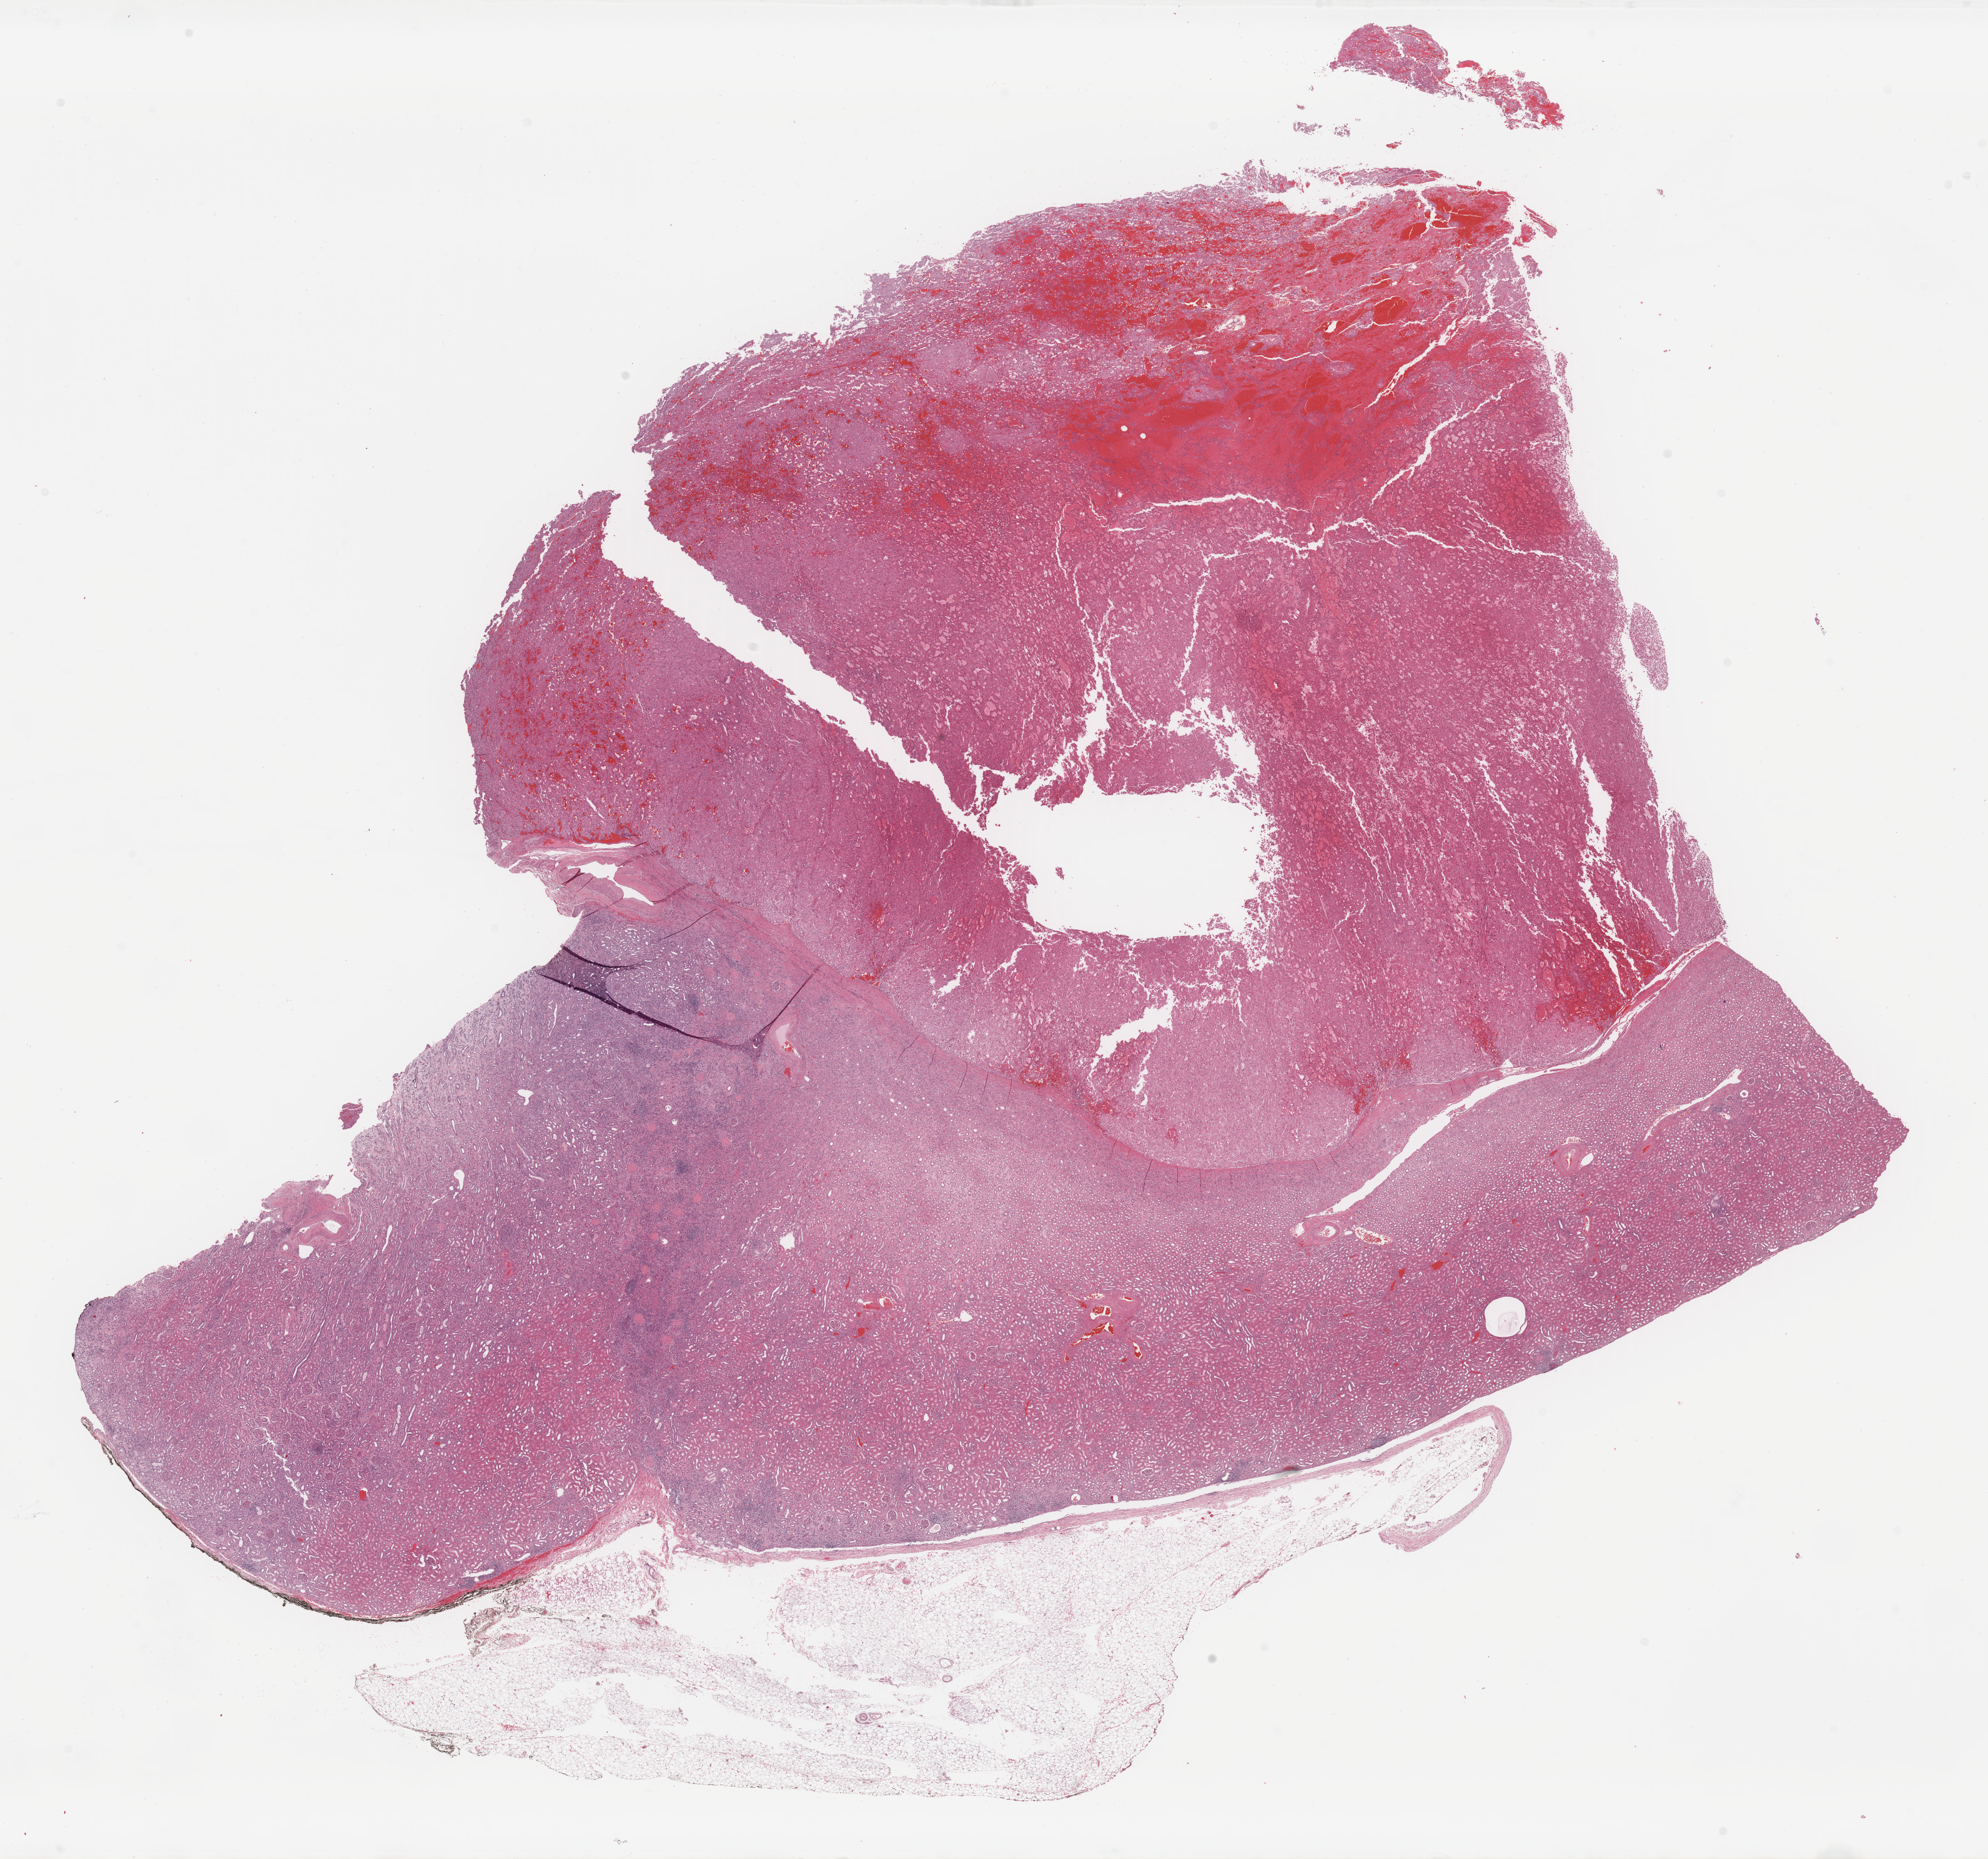
Hematoxylin and eosin (H&E) stained whole-slide image, a low-resolution overview of the entire scanned area, about 25.2 x 23.5 mm; formalin-fixed paraffin-embedded (FFPE) diagnostic section; kidney, primary tumour sample. Female, age 74 years at initial diagnosis. Slide review estimates, as recorded: tumour cells 50%, tumour nuclei 50%, normal cells 30%, stromal cells 20%, necrosis 0%. Inflammatory infiltration, as recorded: lymphocyte infiltration 3%, monocyte infiltration 1%, neutrophil infiltration 1%.
Diagnosis: Renal cell carcinoma, chromophobe type. AJCC pathologic stage: I (6th edition).